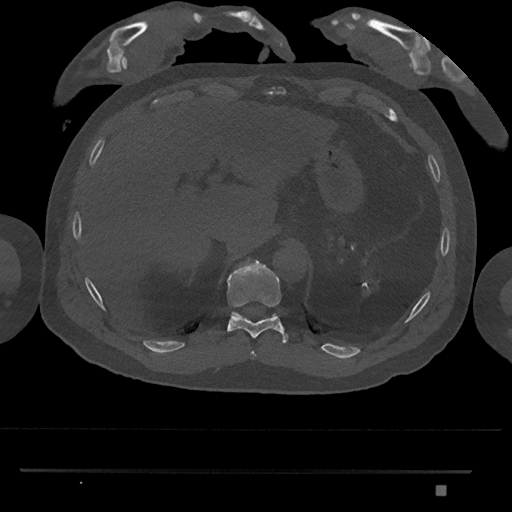
CT including the spine, one axial slice. Position 994 of 1134 along the scan axis. Bone window (W 1800 / L 400 HU). 0.5 mm slice thickness. 512 × 512 image matrix, field of view 429 × 429 mm. Patient: male, 65 years. Case-level facts recorded for this patient, not image findings: primary cancer: prostate.
Outlined on this slice (semi-automatically segmented with operator editing):
- T10 vertebra: bounding box (x1, y1, x2, y2) in pixels: (227, 260, 288, 344)
- T11 vertebra: (232, 312, 277, 318)
- T9 vertebra: (250, 351, 256, 358)